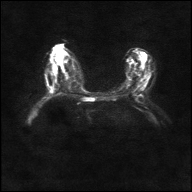
Breast MRI, one axial slice; slice 14 of 36 in the series (ordered by position); diffusion-weighted series; image 2 of 4 stored at this slice position (different b-values; order by instance number); 1.5 T; 192 × 192 image matrix, field of view 360 × 360 mm. Female patient.
Structures marked on this image (outlined manually by an expert reader):
- tumour on diffusion-weighted imaging: bounding box [x1, y1, x2, y2] px = [51, 89, 54, 92]